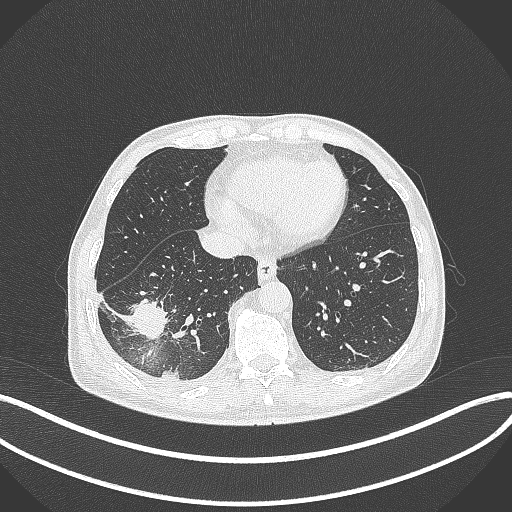
Chest CT, one axial slice; position 108 of 388 along the scan axis; reconstruction kernel B70f; lung window (W 1500 / L -600 HU); 1 mm slice thickness; 512 × 512 image matrix, field of view 400 × 400 mm. Male patient, age 64 years. Case-level facts recorded for this patient, not image findings: clinical TNM (as recorded): T3 N0 M0; histopathological grade: G2-3.
Outlined on this slice (bounding box drawn by a radiologist):
- lung tumour (recorded histology: adenocarcinoma): box from (x=119, y=286) to (x=170, y=348) px